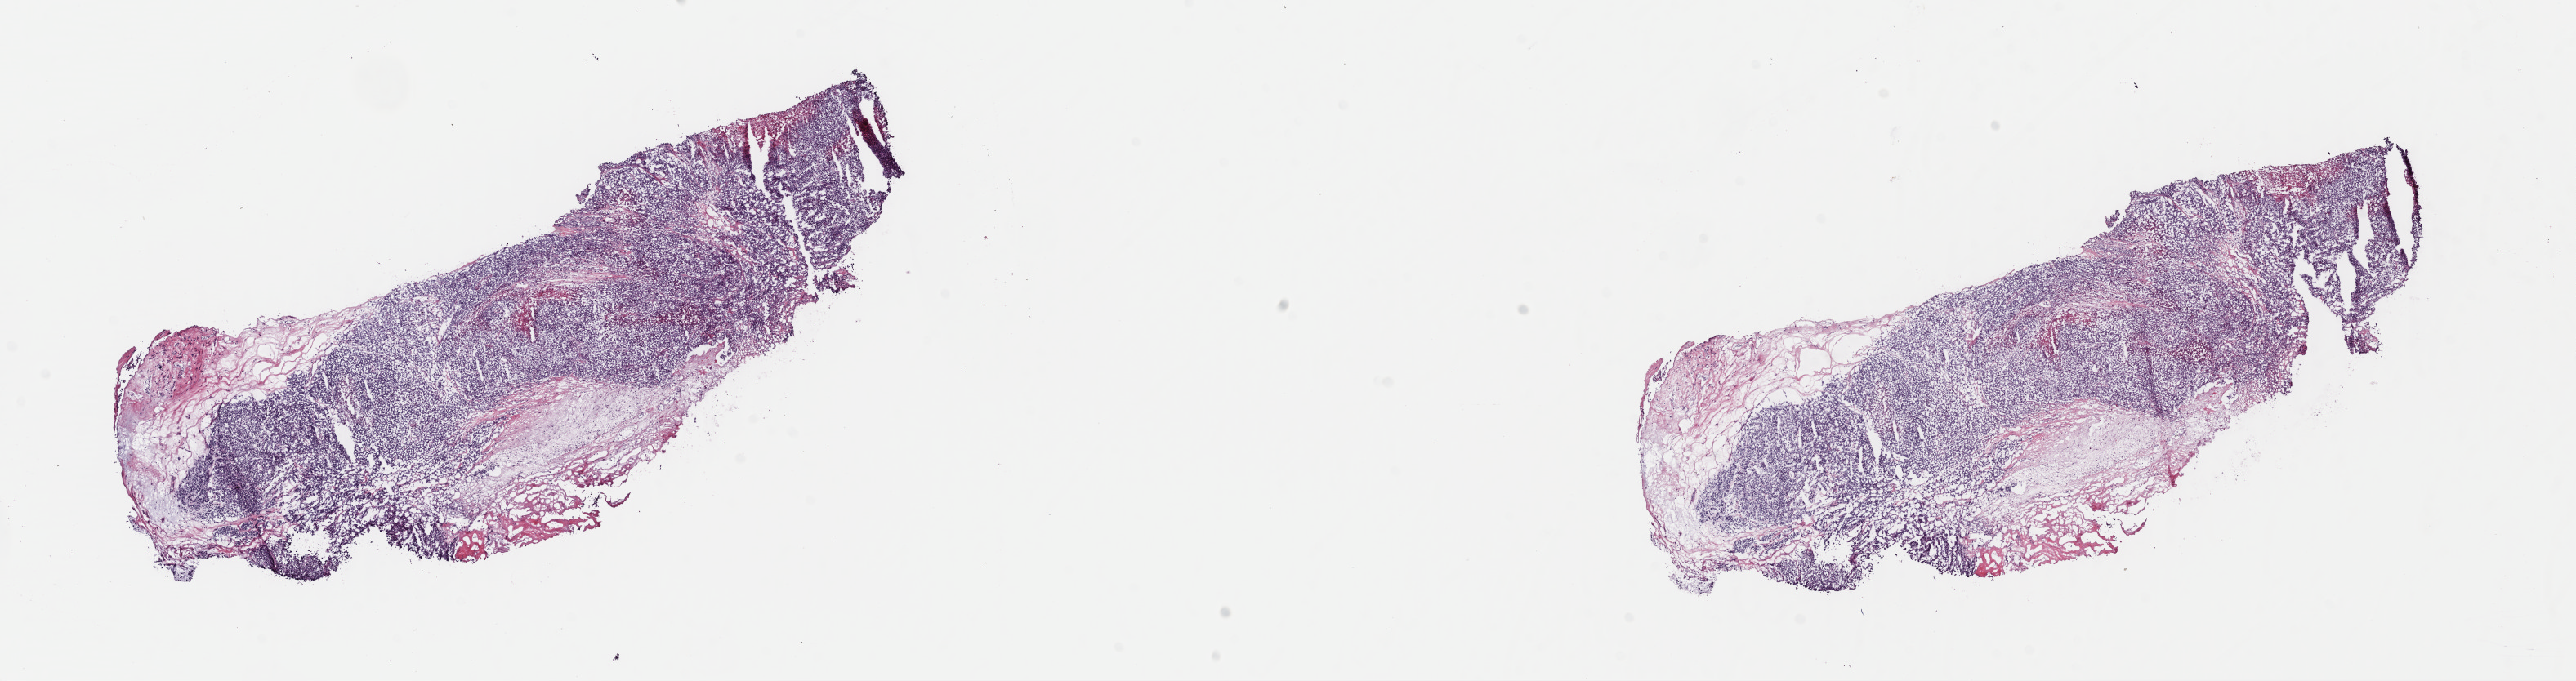
Digitized Hematoxylin and eosin (H&E) stained tissue section (whole slide), a low-resolution overview of the entire scanned area, about 24.8 x 6.6 mm (slide scanned at 40x); frozen section; sample: primary tumour, uterus. Patient: female, age at initial diagnosis 65 years. Composition of this section per pathologist review: tumour cells 70%, tumour nuclei 70%, normal cells 0%, stromal cells 20%, necrosis 10%. Inflammatory infiltration, as recorded: lymphocyte infiltration 20%, monocyte infiltration 20%, neutrophil infiltration 40%.
Histologic diagnosis: Mullerian mixed tumor (endometrium). FIGO stage: IIIC.